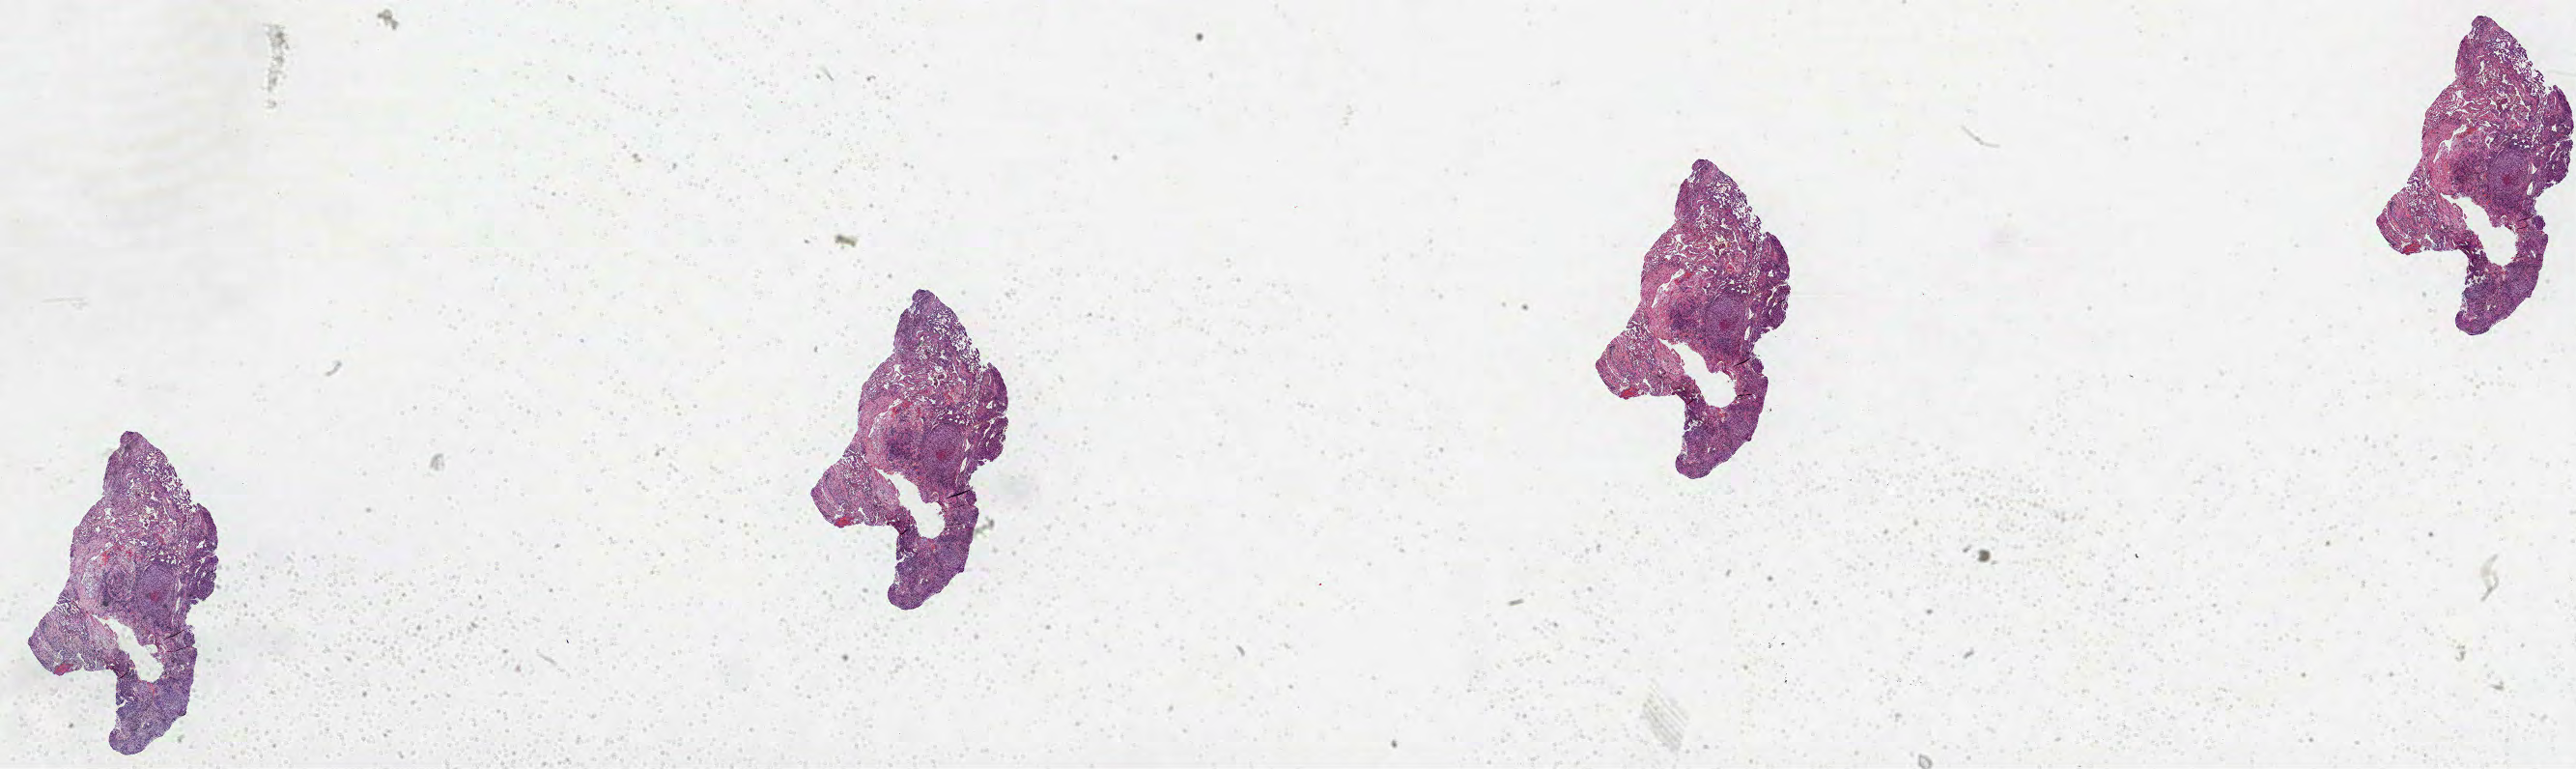
Whole-slide histology image, H&E, whole scanned area (about 43.0 x 12.8 mm, slide scanned at 40x) shown as a low-resolution overview, formalin-fixed paraffin-embedded (FFPE) diagnostic section, lung, primary tumour sample. Female patient; age at initial diagnosis 59 years.
• AJCC pathologic stage: IA
• pathologic diagnosis: Squamous cell carcinoma, NOS (upper lobe, lung)